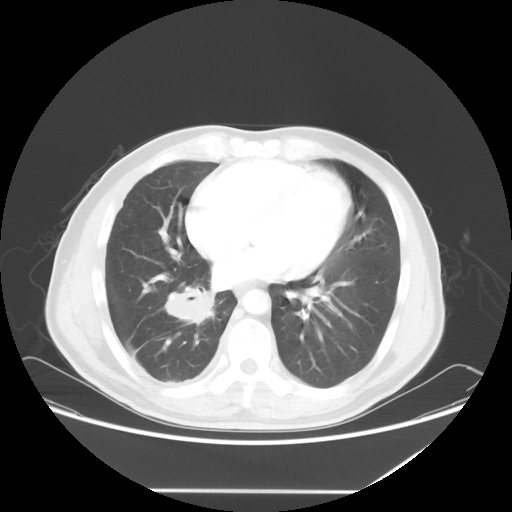
Chest CT, one axial slice; position 24 of 60 along the scan axis; 120 kVp; lung window (W 1500 / L -600 HU); 5 mm slice thickness; 512 × 512 image matrix, field of view 419 × 419 mm. Male patient, age 48 years. Case-level facts recorded for this patient, not image findings: clinical TNM (as recorded): T3 N3 M1a.
Structures marked on this image (rectangle marked by the reading radiologist):
- lung tumour (recorded histology: squamous cell carcinoma): box from (x=162, y=282) to (x=219, y=332) px